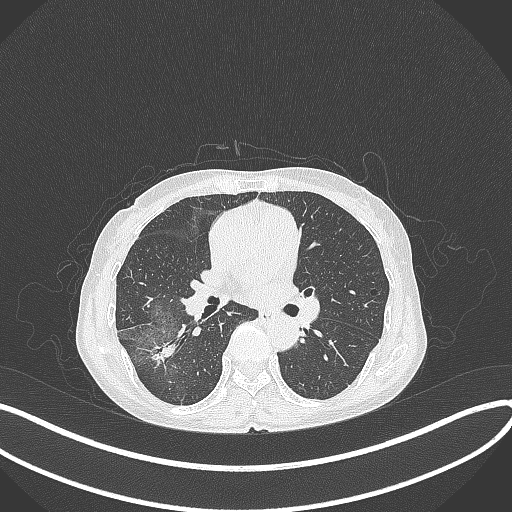
Chest CT, one axial slice. Slice 213 of 371 in the series (ordered by position). Reconstruction kernel B70f. Lung window (W 1500 / L -600 HU). 512 × 512 image matrix, field of view 400 × 400 mm. Patient: female, 69 years. Case-level facts recorded for this patient, not image findings: clinical TNM (as recorded): T1b N0 M0; histopathological grade: G2-3.
Annotated regions visible in this slice (bounding box drawn by a radiologist):
- lung tumour (recorded histology: adenocarcinoma): box from (x=147, y=339) to (x=183, y=364) px